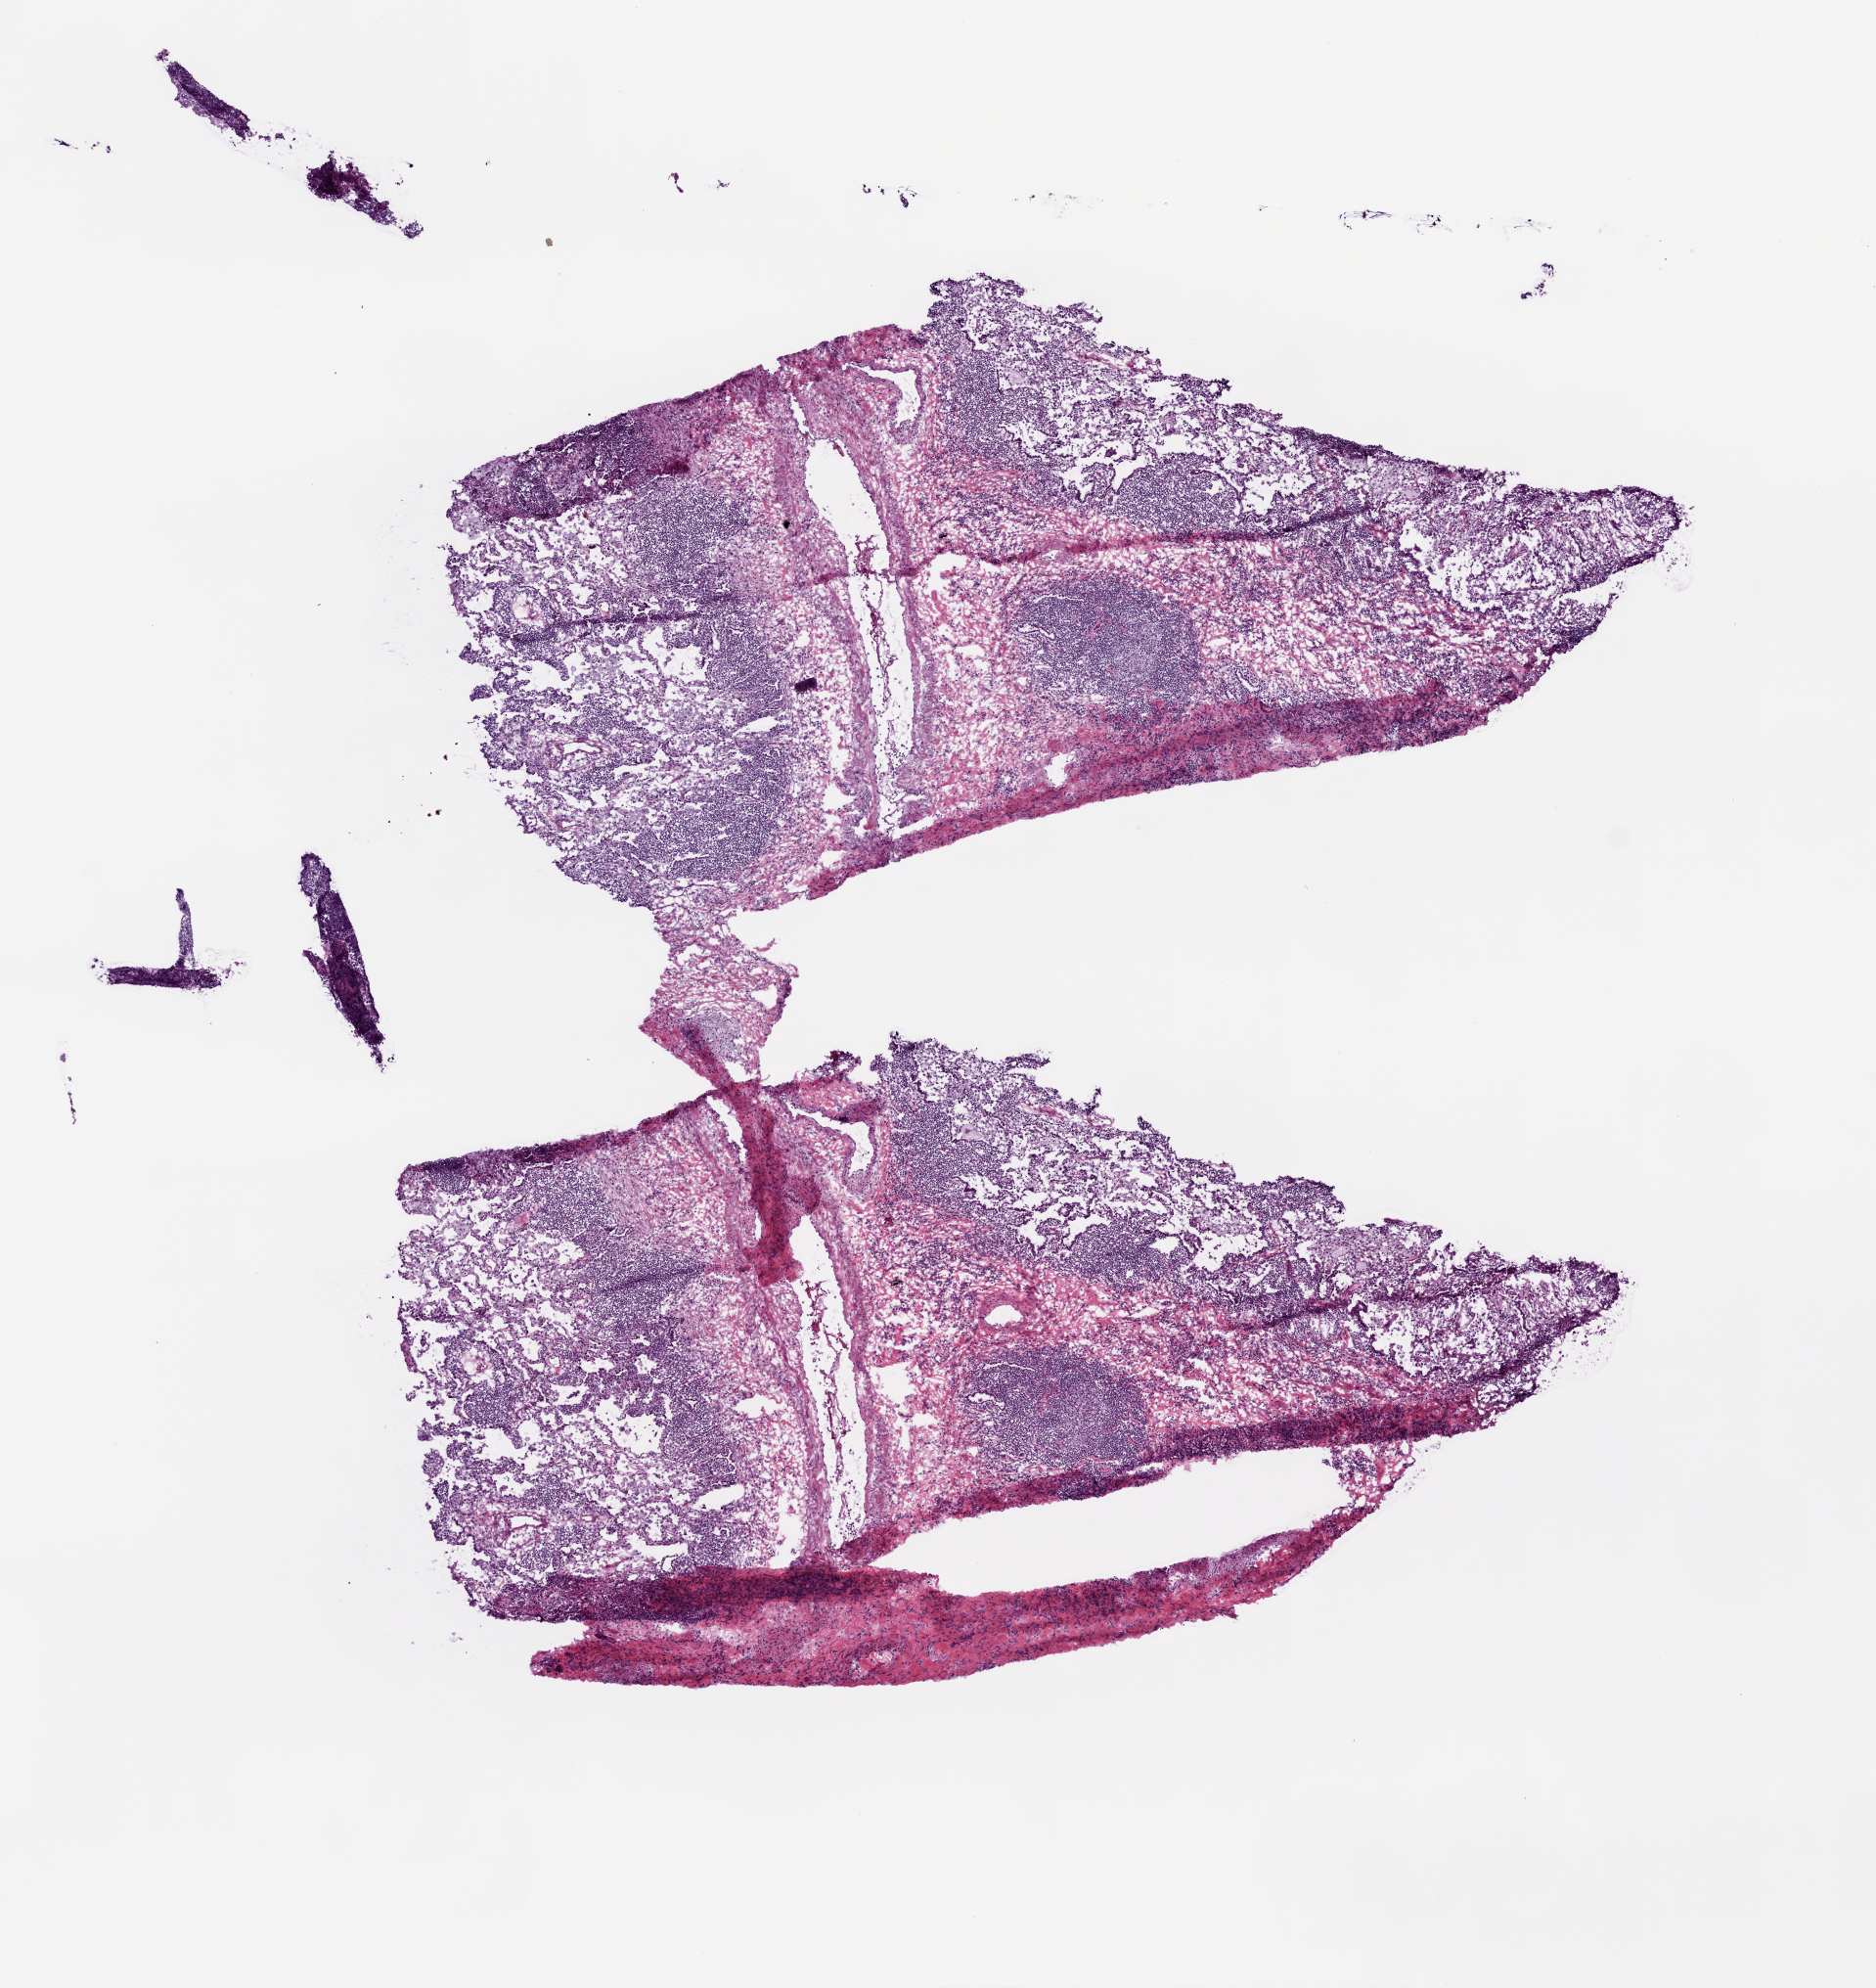
Digitized Hematoxylin and eosin (H&E) stained tissue section (whole slide), a low-resolution overview of the entire scanned area, about 7.7 x 8.2 mm (from a 20x scan). Frozen section. Sample: primary tumour, lung. Patient: male, age at initial diagnosis 57 years. Slide review estimates, as recorded: tumour cells 10%, tumour nuclei 10%, normal cells 90%, stromal cells 0%, necrosis 0%.
• TNM: T3 N0 M0
• AJCC pathologic stage: IIB
• laterality: left
• pathologic diagnosis: Squamous cell carcinoma, NOS (upper lobe, lung)